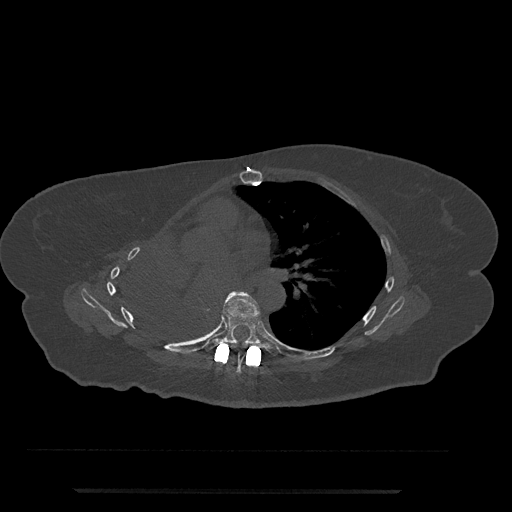
CT including the spine, one axial slice; slice 463 of 797 in the series (ordered by position); 120 kVp; bone window (W 1800 / L 400 HU); 0.5 mm slice thickness; 512 × 512 image matrix. Female patient, age 51 years. From the clinical record (not read from this slice): primary cancer: neuro; vertebrae with lytic lesions (as recorded): T8.
Outlined on this slice (semi-automatic segmentation, software-assisted and operator-edited):
- T6 vertebra: box from (x=227, y=351) to (x=245, y=373) px
- T7 vertebra: (x=204, y=292)–(x=278, y=356)